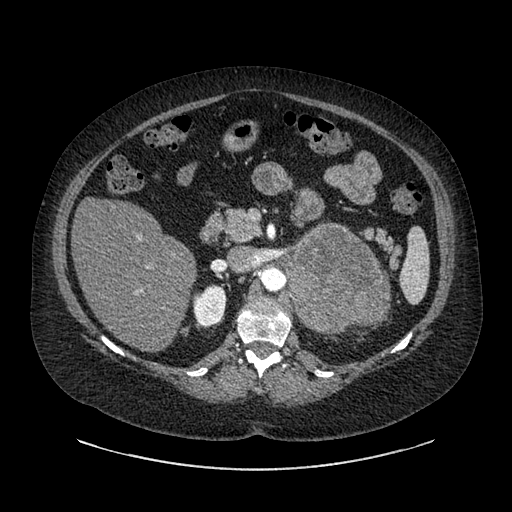
Contrast-enhanced abdominal CT, one axial slice. Position 548 of 769 along the scan axis. Reconstruction kernel SOFT. Intravenous contrast given. Soft-tissue window (W 400 / L 40 HU). 0.62 mm slice thickness. 512 × 512 image matrix. Patient: female, 61 years. Case-level facts recorded for this patient, not image findings: diagnosis: adrenocortical carcinoma; tumour side: left adrenal; tumour size at pathology: 13 cm; Ki-67 index: 79 %; stage (as recorded): 2.
Annotated regions visible in this slice (semi-automatic segmentation, software-assisted and operator-edited):
- mass: bounding box <289,227,386,333> (left, top, right, bottom; pixels)